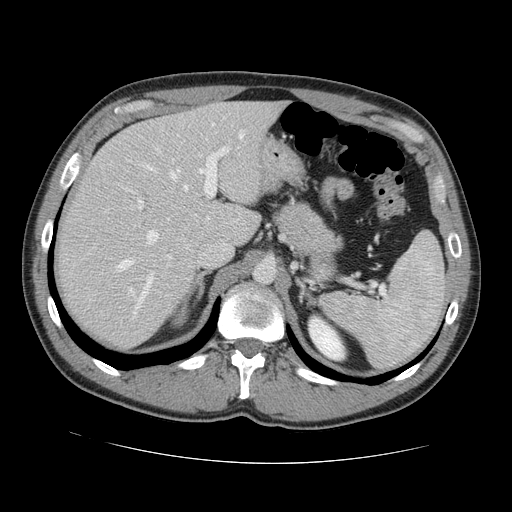
Contrast-enhanced abdominal CT, one axial slice. Slice 92 of 131 in the series (ordered by position). 120 kVp. Soft-tissue window (W 400 / L 40 HU). 2.5 mm slice thickness. 512 × 512 image matrix, field of view 380 × 380 mm. Male patient, age 40 years. From the clinical record (not read from this slice): diagnosis: colorectal cancer liver metastases, imaged before liver resection; multiple liver metastases: yes; largest metastasis: 2.9 cm; disease in both lobes: yes.
Annotated regions visible in this slice (outlined manually by an expert reader):
- hepatic veins: box from (x=118, y=135) to (x=243, y=315) px
- liver: (x=60, y=101)–(x=282, y=348)
- planned liver remnant (the part of the liver to remain after resection): (x=99, y=102)–(x=283, y=245)
- portal vein (with intrahepatic branches): (x=94, y=147)–(x=229, y=296)